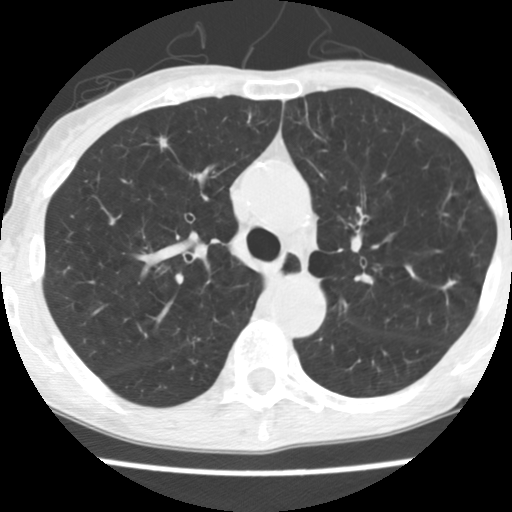
Axial slice from a low-dose chest CT screening exam; baseline screening round; lung window (W 1500 / L -600 HU); 2.5 mm slice thickness; standard (soft-tissue) reconstruction kernel (STANDARD); 120 kVp. Female participant, aged 70 years at enrolment.
Lesion marked by an expert reader, bounding box [x1, y1, x2, y2] px = [132, 121, 188, 169]. No non-calcified nodule or mass ≥4 mm was recorded by the screening reader at this exam. Official screen result: negative screen, significant abnormalities not suspicious for lung cancer. Participant outcome: lung cancer diagnosed 226 days after this screen — large cell neuroendocrine carcinoma, right upper lobe, stage IA (AJCC 6th edition), 30 mm at pathology.